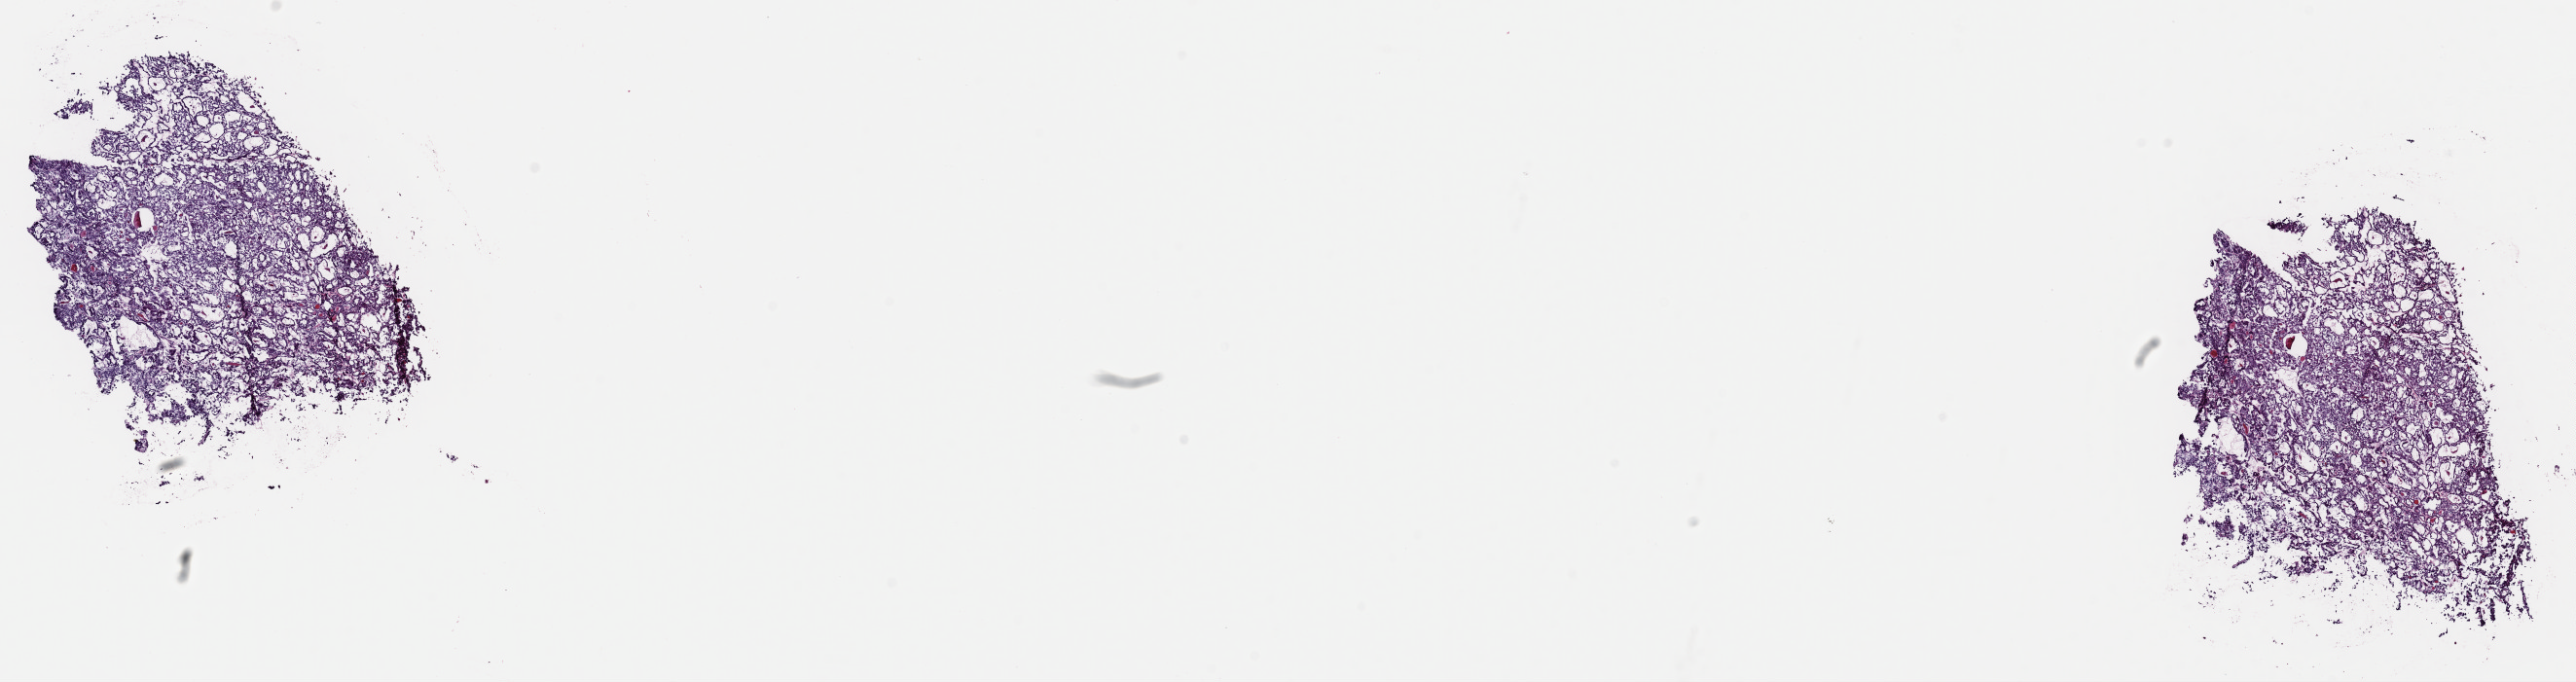
Digitized H&E-stained tissue section (whole slide) — shown as a low-resolution overview of the whole scanned area (about 20.9 x 5.5 mm, acquisition: 40x scan); frozen section from the top of the tissue portion; sample: primary tumour, thyroid. Female, age 37 years at initial diagnosis. Slide review estimates, as recorded: tumour cells 100%, tumour nuclei 85%, normal cells 0%, stromal cells 0%, necrosis 0%. Inflammatory infiltration, as recorded: lymphocyte infiltration 0%, monocyte infiltration 0%, neutrophil infiltration 0%.
• laterality: left
• pathologic diagnosis: Papillary carcinoma, follicular variant
• lymph nodes positive (case pathology): 0 of 1 examined
• AJCC pathologic stage: I (6th edition)